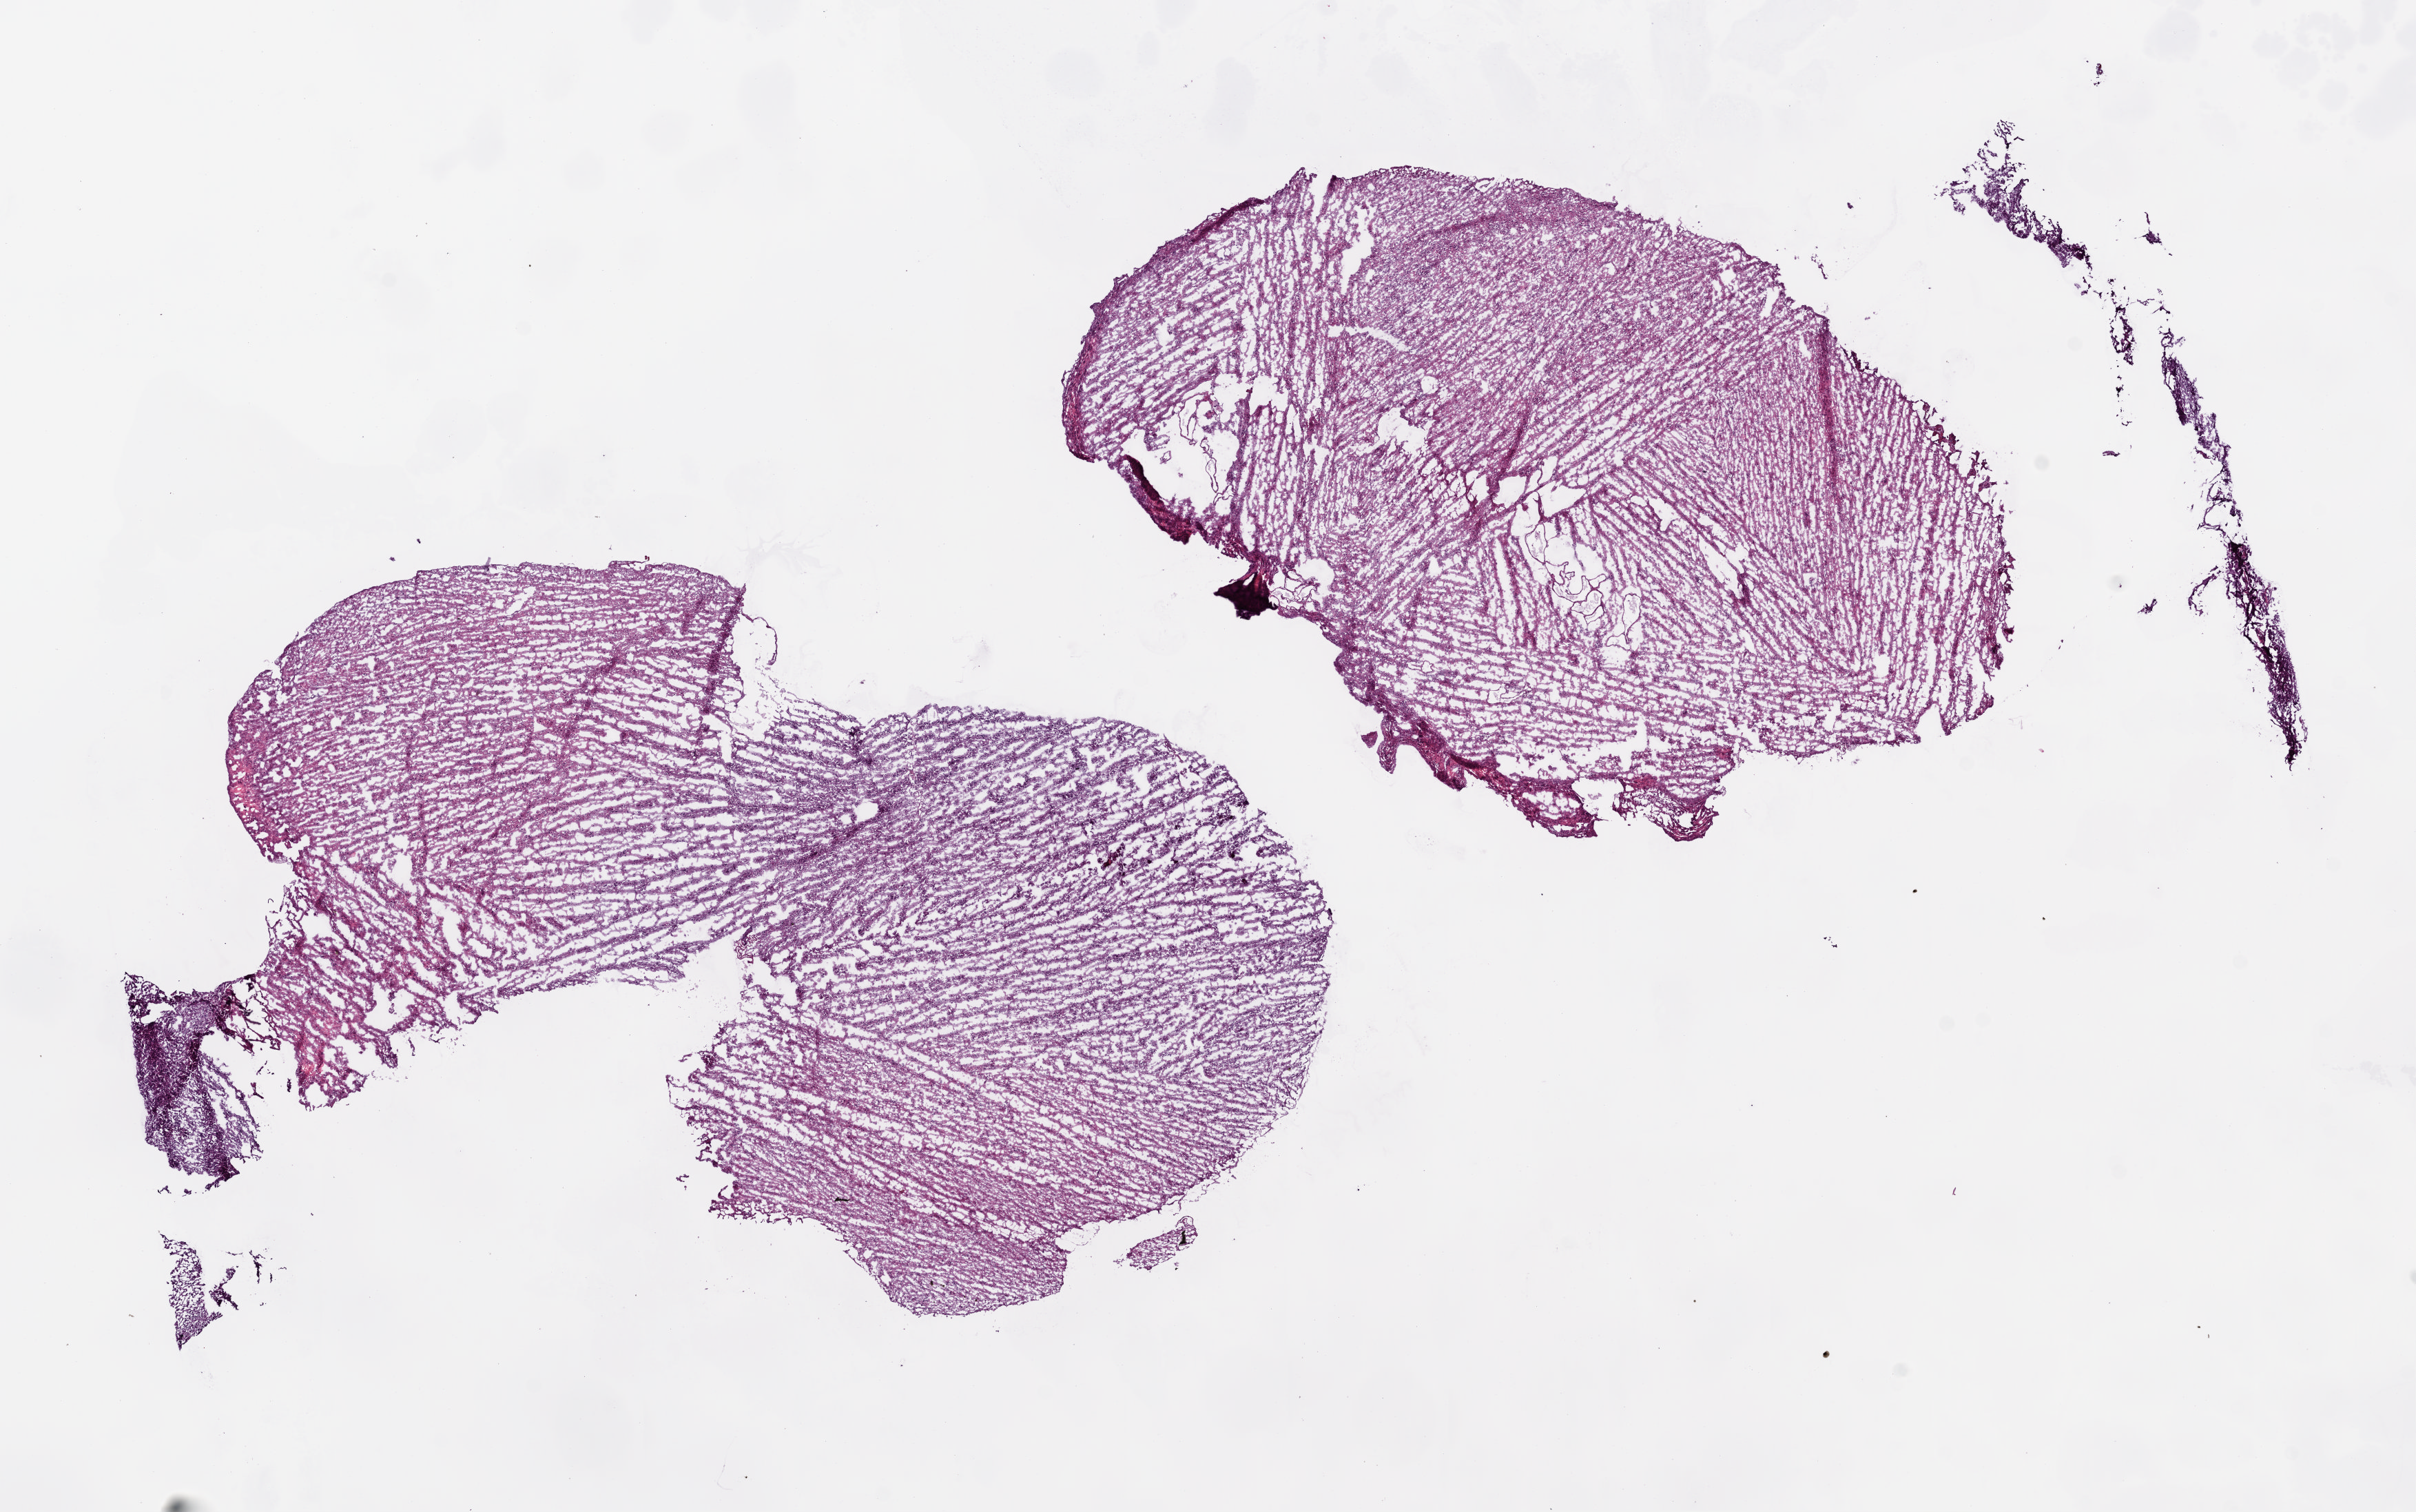
Digitized Hematoxylin and eosin (H&E) stained tissue section (whole slide), shown as a low-resolution overview of the whole scanned area (about 14.1 x 8.8 mm, acquisition: 5x scan). Frozen section. Sample: primary tumour, brain. Female patient; age at initial diagnosis 47 years. Histologic grade: G2 (moderately differentiated). Pathologist review of this section (percent, as recorded): tumour cells 100%, tumour nuclei 75%, normal cells 0%, stromal cells 0%, necrosis 0%.
Pathologic diagnosis: Oligodendroglioma, NOS.